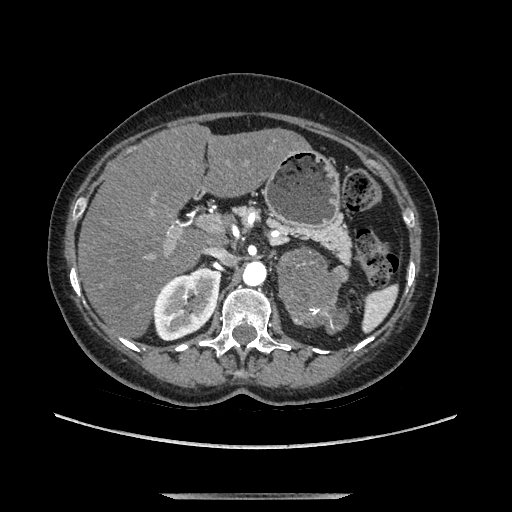
Contrast-enhanced abdominal CT, one axial slice; slice 73 of 169 in the series (ordered by position); soft-tissue window (W 400 / L 40 HU); 512 × 512 image matrix. Female patient. From the clinical record (not read from this slice): diagnosis: adrenocortical carcinoma; tumour side: left adrenal; tumour size at pathology: 9 cm; Ki-67 index: 2 %; stage (as recorded): 3.
Structures marked on this image (semi-automatically segmented with operator editing):
- mass: bounding box (x1, y1, x2, y2) in pixels: (279, 253, 344, 331)